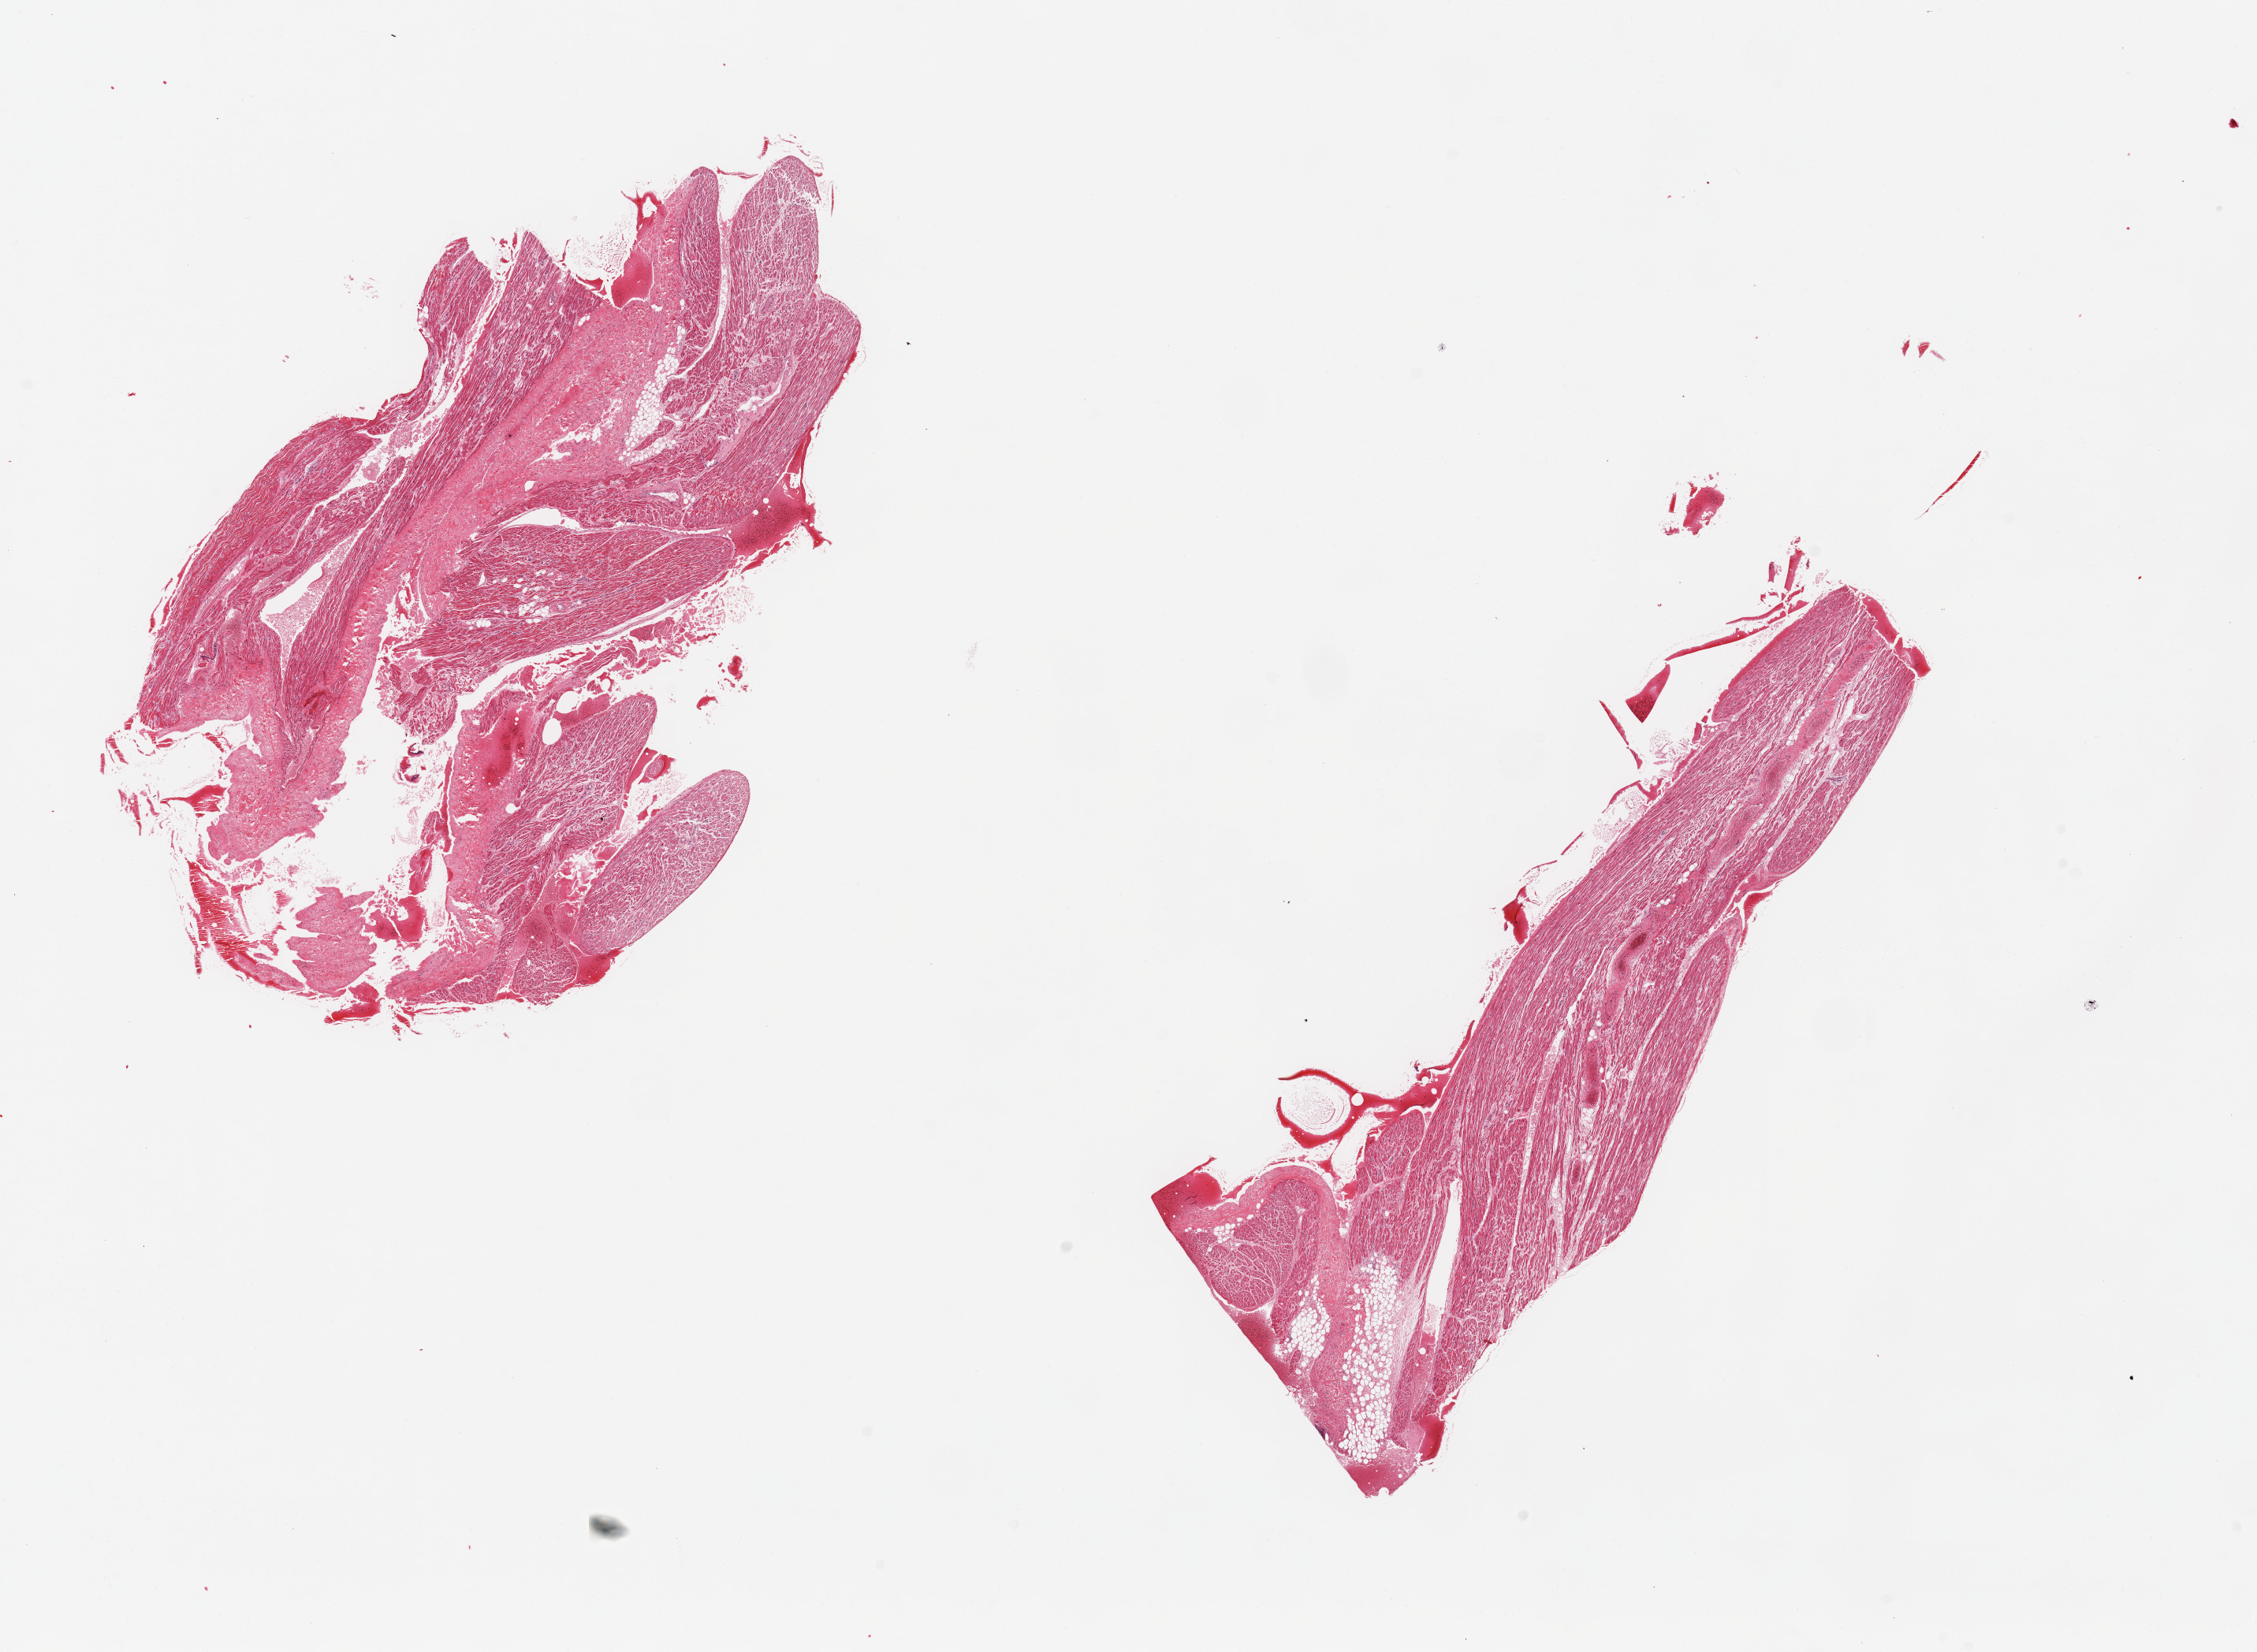
Whole-slide image, H&E stain, shown as a low-resolution overview of the whole scanned area (about 22.6 x 16.6 mm); PAXgene-fixed paraffin-embedded (PFPE) section; section of auricular appendage (target tissue); donor tissue sample. Donor: male.
Review note (as recorded): 2 pieces; 20 & 5% fat and fibrous tissue.